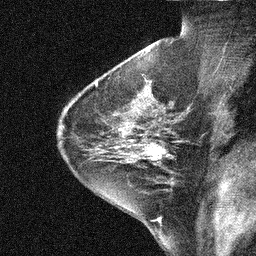
Breast MRI (dynamic contrast-enhanced), one sagittal slice; position 30 of 44 along the scan axis; dynamic contrast-enhanced study with each time point stored as its own series, time point 2 of 3 at this slice position (early post-contrast, ordered by acquisition time); 1.5 T; TE 5 ms, TR 10.3 ms; 3 mm slice thickness; 256 × 256 image matrix. Female patient, age 31 years. Case-level facts recorded for this patient, not image findings: setting: breast cancer imaged before/during neoadjuvant chemotherapy; receptor status: HER2-positive.
Outlined on this slice (semi-automatically segmented with operator editing):
- analysis volume of interest (the breast-tissue region the enhancement analysis was run in; not a lesion): bounding box <136,131,181,168> (left, top, right, bottom; pixels)
- tumour enhancement mask (voxels above the 90 % enhancement threshold inside the analysis volume of interest): <143,142,169,160>